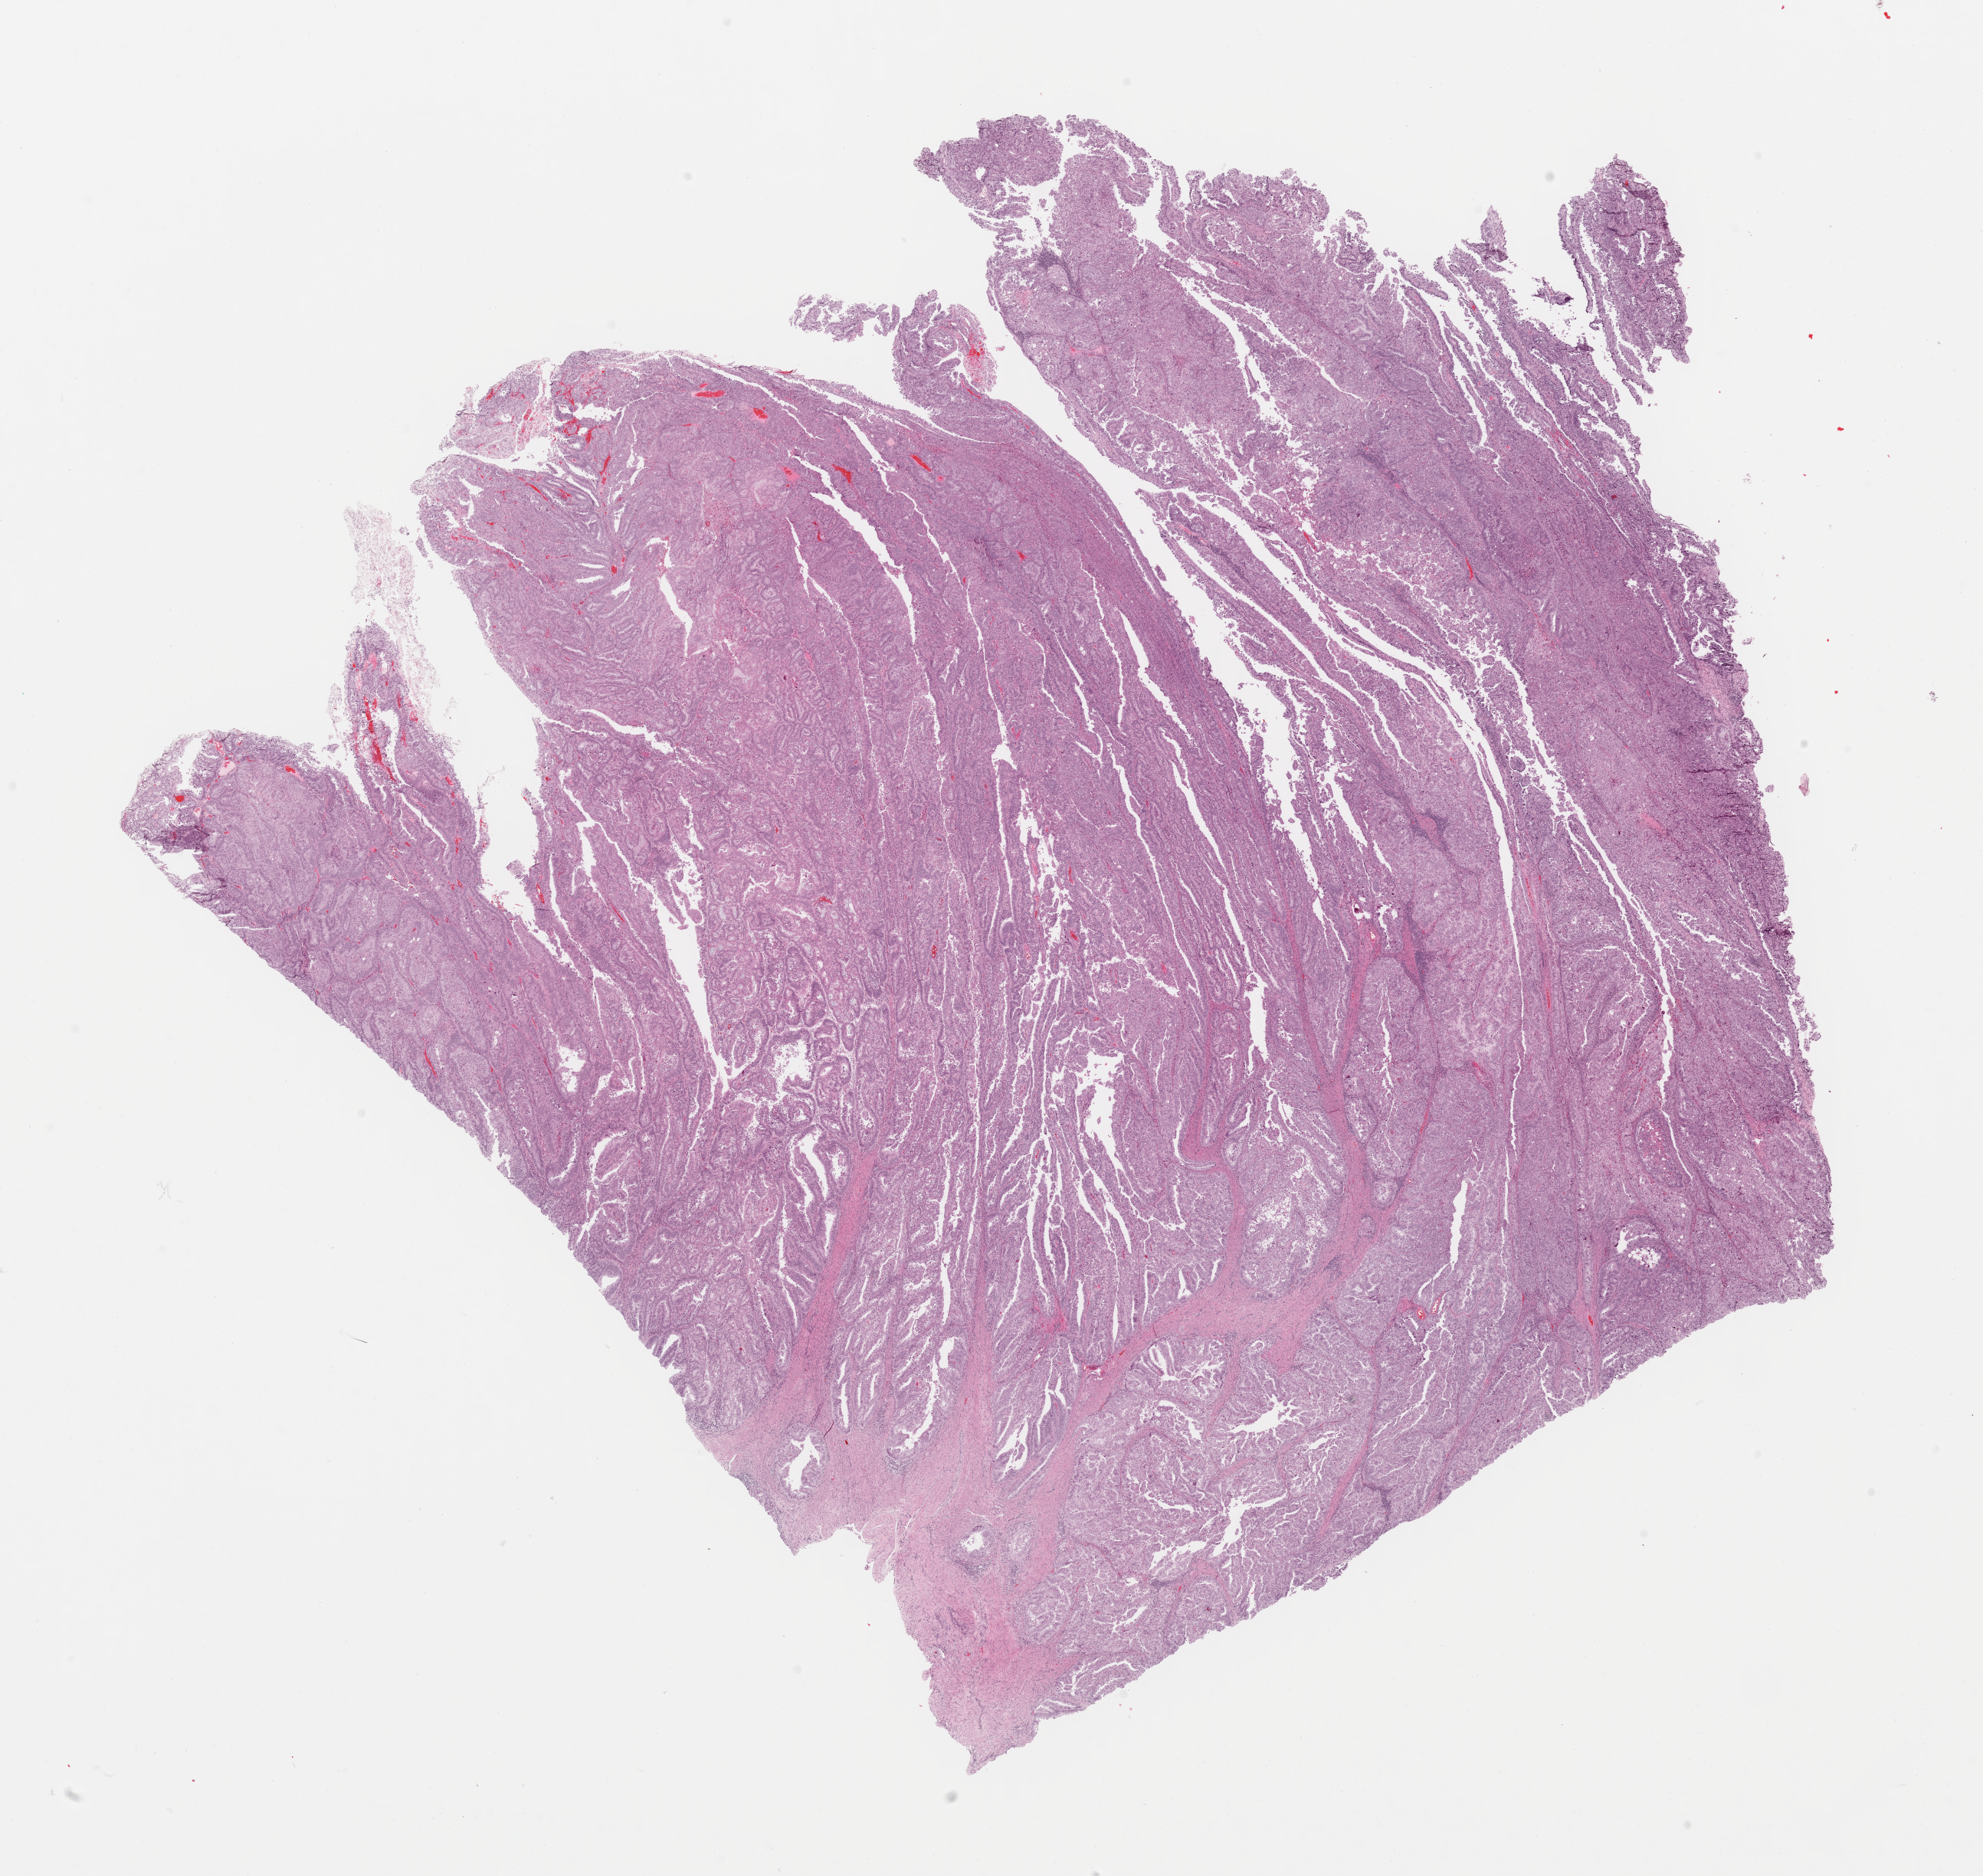
Whole-slide histology image, Hematoxylin and eosin (H&E) stained — a low-resolution overview of the entire scanned area, about 20.4 x 19.3 mm. FFPE section. Sample: primary tumour, uterus. Female, age 66 years at initial diagnosis. Histologic grade: G3 (poorly differentiated).
FIGO stage: IB. Histologic diagnosis: Serous cystadenocarcinoma, NOS (endometrium).